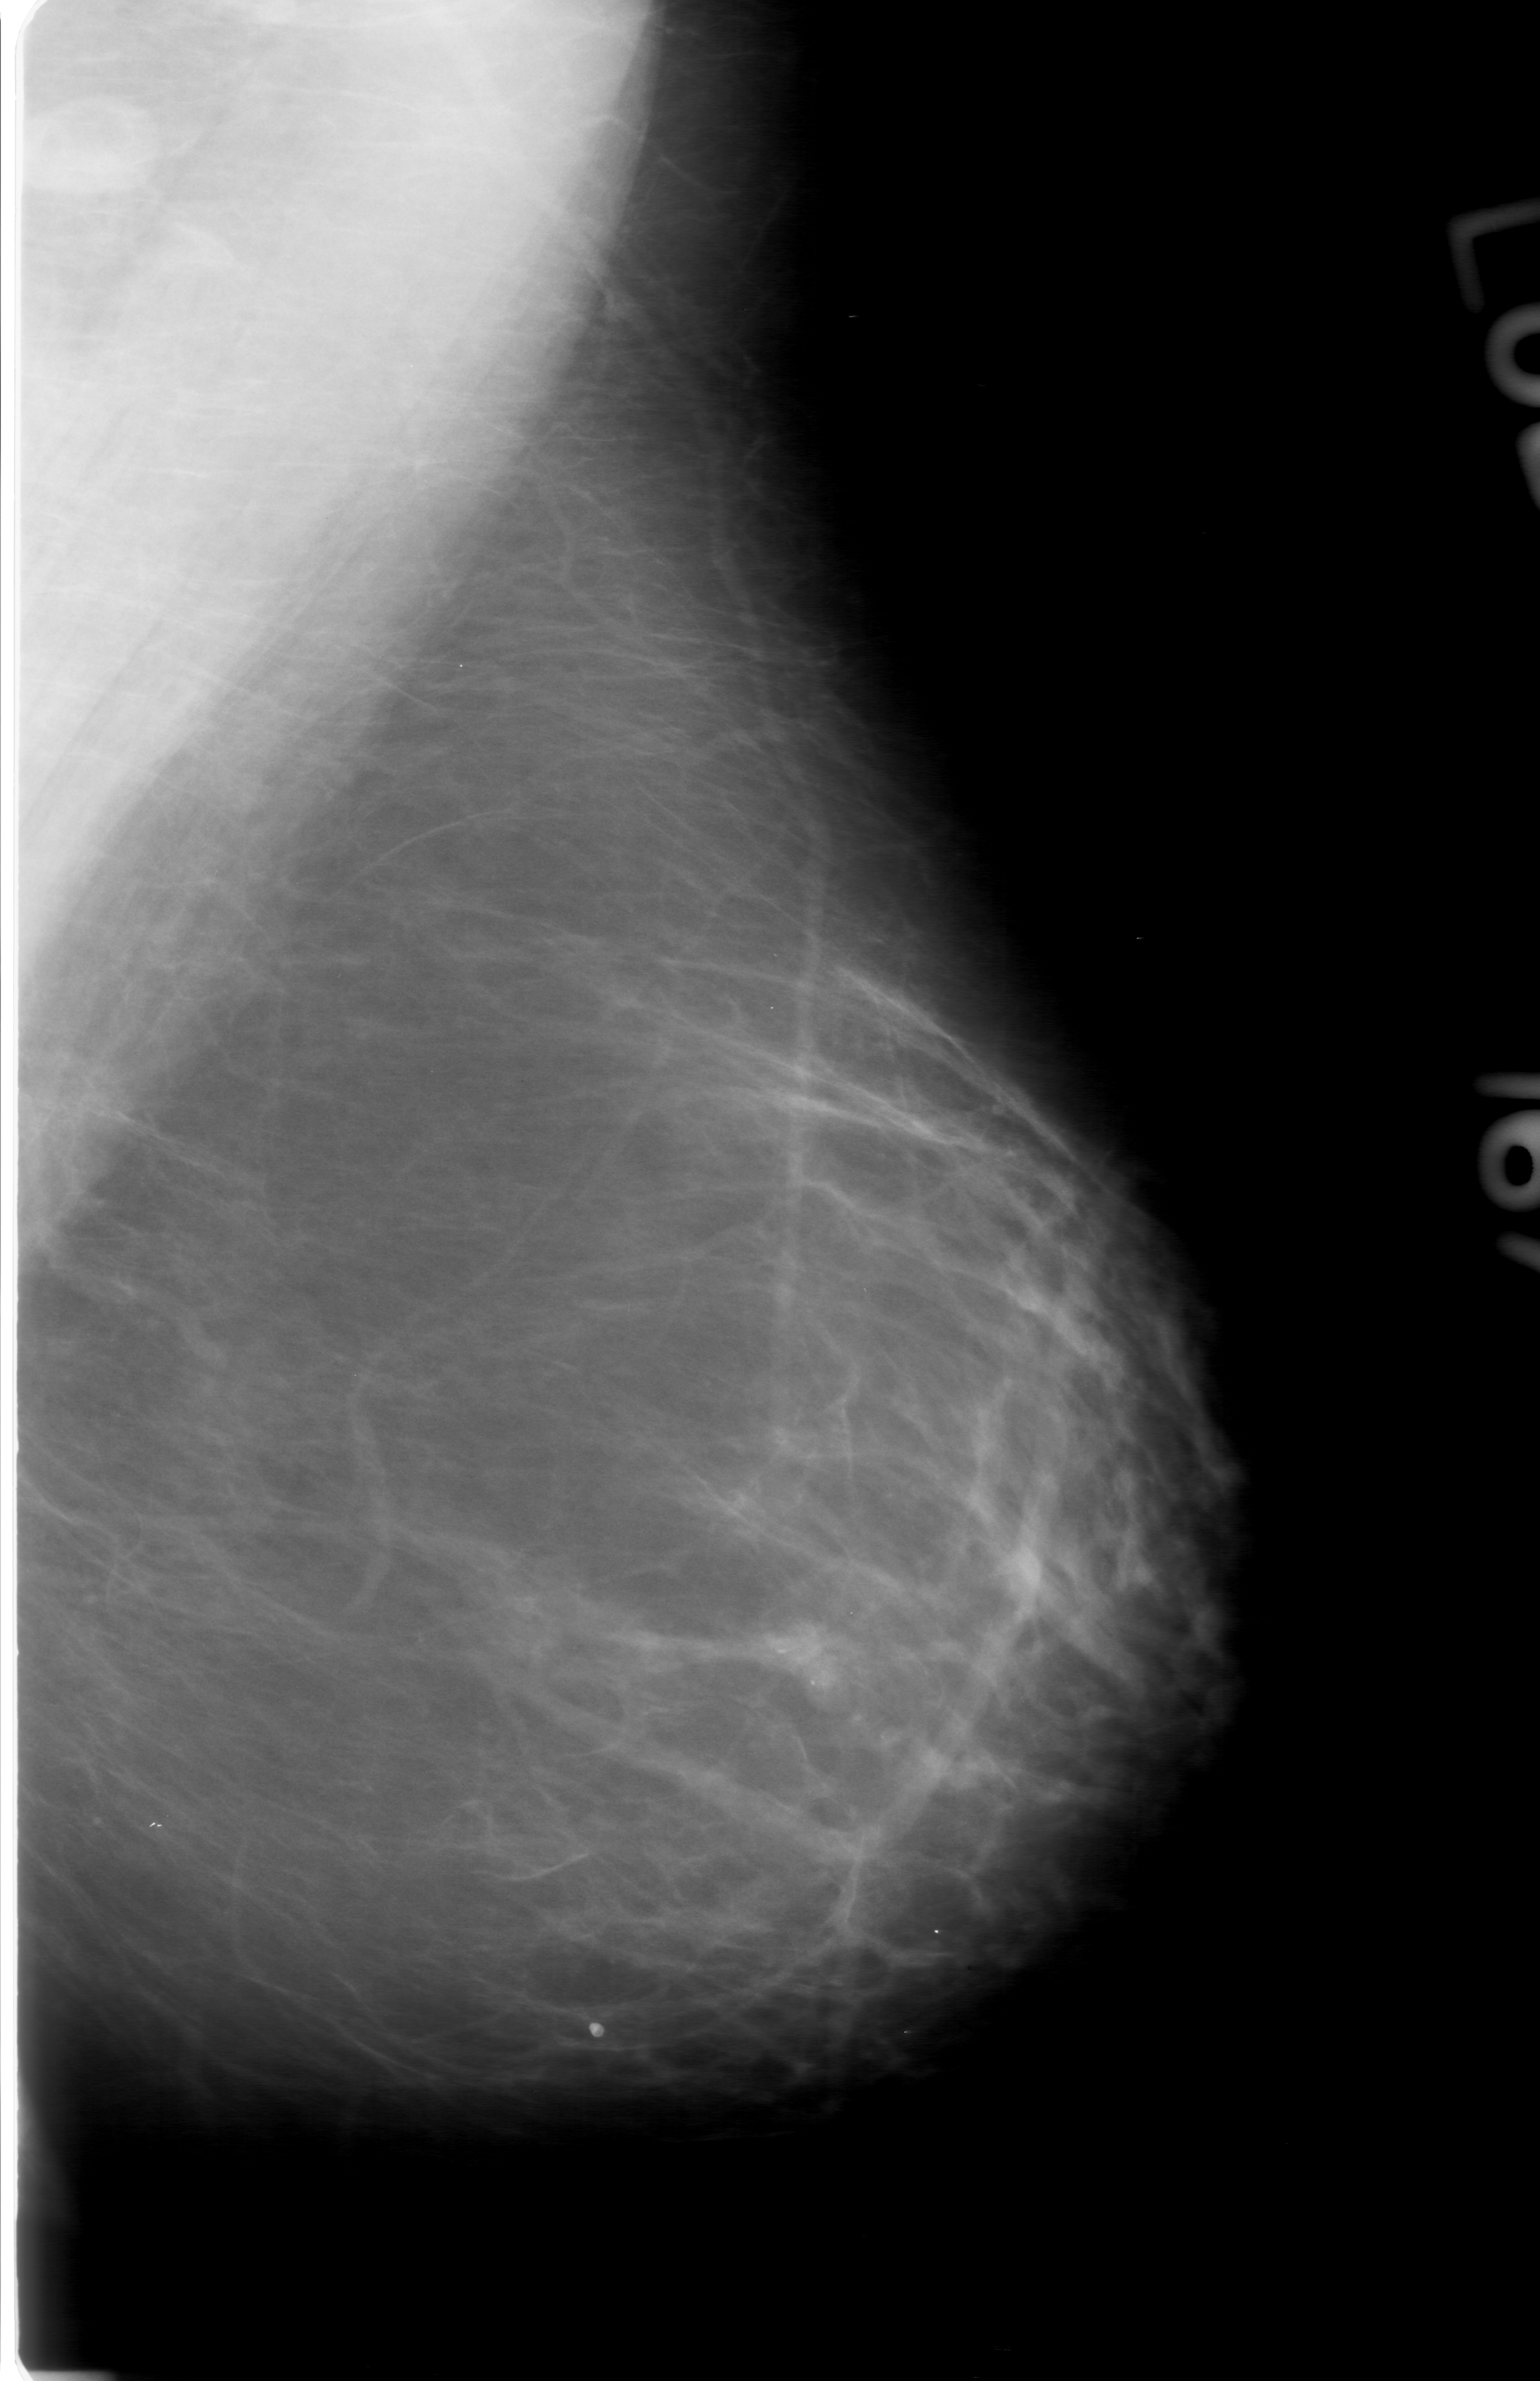
Mammogram (digitized film). Left breast. MLO view. Breast composition: almost entirely fatty (BI-RADS density category 1 of 4). 1540 × 2381 image matrix.
Expert-marked regions of interest on this film, with their recorded descriptors:
- calcifications, morphology fine linear branching, distribution clustered; BI-RADS assessment category 3; subtlety rating 2 on a 1 (subtle) to 5 (obvious) scale; pathology result (as recorded, not read from the image): malignant: bounding box (x1, y1, x2, y2) in pixels: (642, 1513, 1020, 1871)